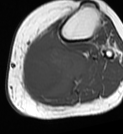
MRI of an extremity soft-tissue mass, one axial slice; position 37 of 68 along the scan axis; MR volume resampled by the dataset authors to the PET/CT grid (not the native acquisition matrix); 3.27 mm slice thickness; 123 × 134 image matrix, field of view 120 × 131 mm. Female patient. From the clinical record (not read from this slice): histological type: extraskeletal high grade osteogenic sarcoma; grade: high; site of the primary tumour: left calf.
Outlined on this slice (expert contour drawn on MRI and transferred to this co-registered scan by the dataset authors):
- gross tumour volume (mass): bounding box [x1, y1, x2, y2] px = [22, 32, 87, 97]